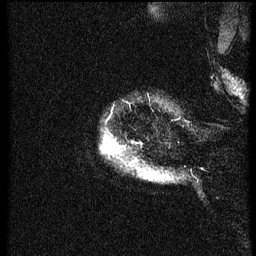
Breast MRI (dynamic contrast-enhanced), one sagittal slice; slice 57 of 60 in the series (ordered by position); dynamic contrast-enhanced series, image 2 of 3 at this slice position (ordered by acquisition); 1.5 T; TE 4.2 ms, TR 8.4 ms; 2.5 mm slice thickness; 256 × 256 image matrix, field of view 200 × 200 mm. Patient: female, 38 years. From the clinical record (not read from this slice): setting: breast cancer imaged before/during neoadjuvant chemotherapy; receptor status: HER2-positive.
Structures marked on this image (semi-automatically segmented with operator editing):
- analysis volume of interest (the breast-tissue region the enhancement analysis was run in; not a lesion): bounding box (x1, y1, x2, y2) in pixels: (105, 141, 173, 182)
- tumour enhancement mask (voxels above the 70 % enhancement threshold inside the analysis volume of interest): (106, 146, 112, 151)